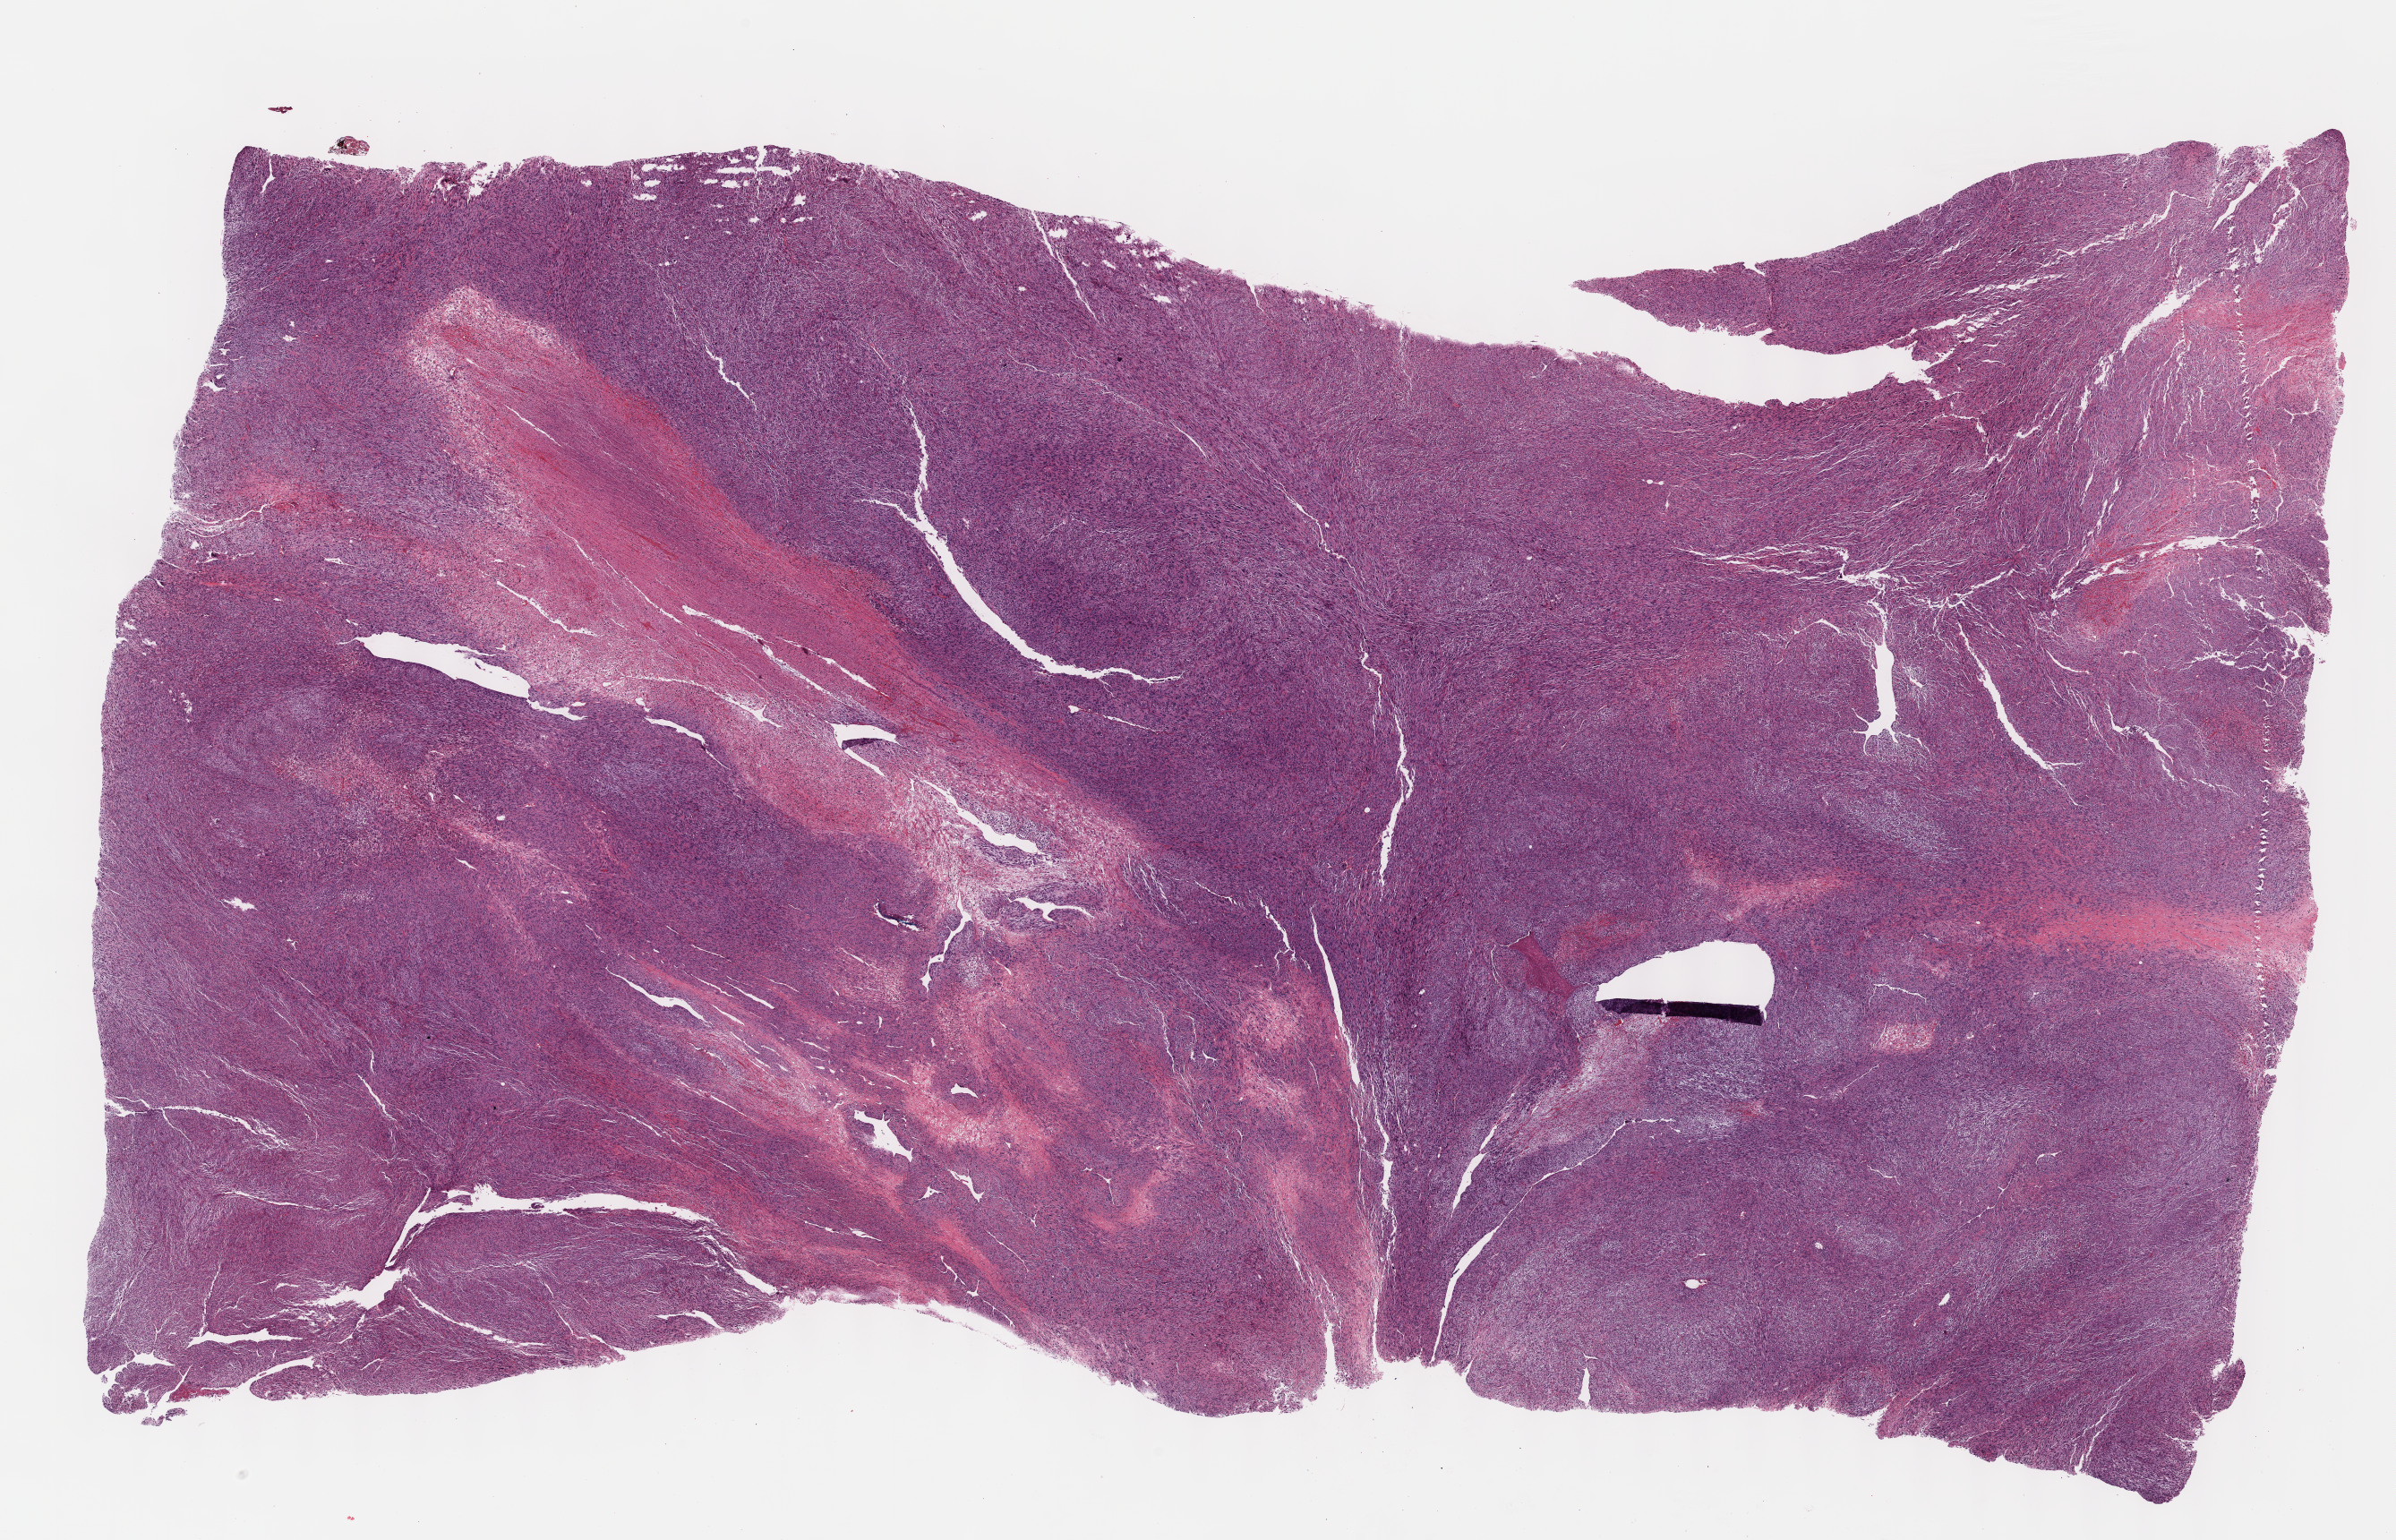
Whole-slide histology image, H&E-stained, shown as a low-resolution overview of the whole scanned area (about 21.6 x 13.9 mm); formalin-fixed paraffin-embedded (FFPE) diagnostic section; connective, subcutaneous and other soft tissues, primary tumour sample. Patient: female, age at initial diagnosis 68 years.
* pathologic diagnosis: Fibromyxosarcoma (connective, subcutaneous and other soft tissues of lower limb and hip)